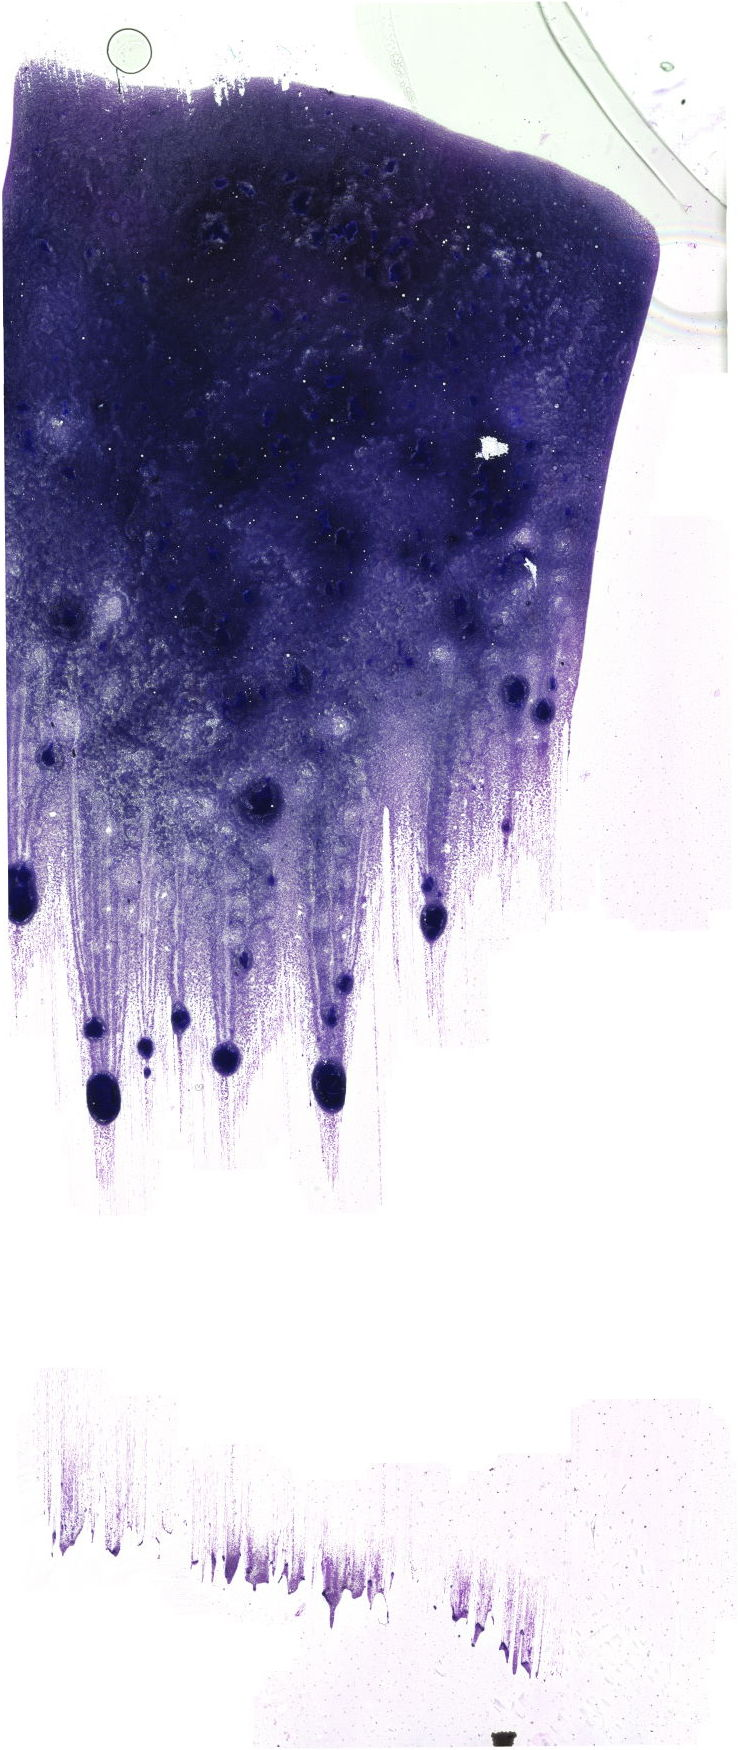
Whole-slide image of a May-Grünwald–Giemsa-stained bone marrow aspirate smear, low-resolution overview of the scanned area, about 20.9 x 49.6 mm. Patient sex: female.
Diagnosis: Chronic Phase Chronic Myeloid Leukemia, BCR-ABL1 Positive.